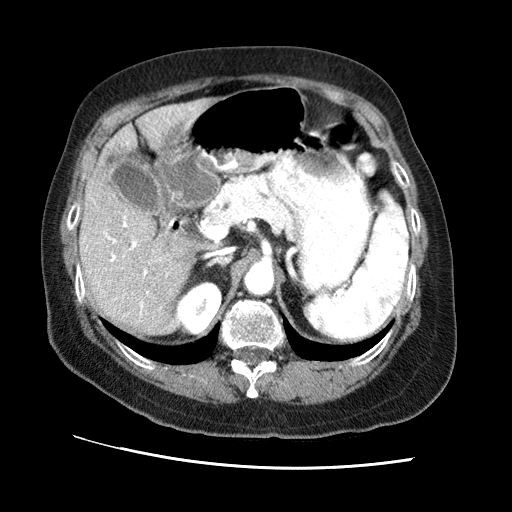
Contrast-enhanced abdominal CT (liver protocol), one axial slice; reconstruction kernel STANDARD; 120 kVp; soft-tissue window (W 400 / L 40 HU); 2.5 mm slice thickness; 512 × 512 image matrix, field of view 340 × 340 mm. Case-level facts recorded for this patient, not image findings: diagnosis: hepatocellular carcinoma (patient treated with transarterial chemoembolisation; whether this scan precedes or follows treatment is not stated here); TNM stage (as recorded): Stage-II; Child-Pugh class: A; tumour differentiation: no biopsy.
Outlined on this slice (semi-automatic segmentation, software-assisted and operator-edited):
- liver parenchyma outside the tumour (the mass and vessels are separate outlines, so this box may not span the whole liver): bounding box <80,98,212,334> (left, top, right, bottom; pixels)
- liver vessels: <103,108,193,315>